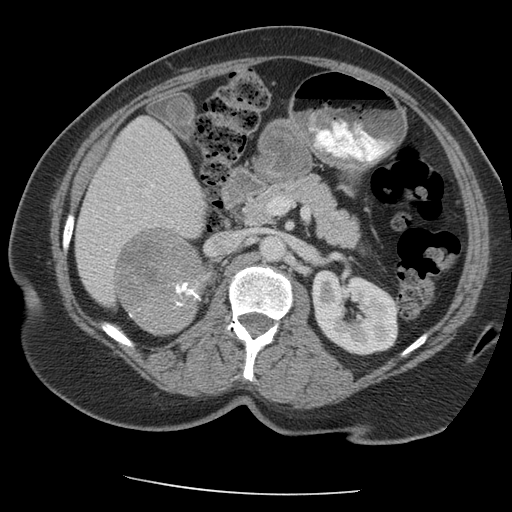
Contrast-enhanced abdominal CT, one axial slice; slice 115 of 163 in the series (ordered by position); reconstruction kernel STANDARD; intravenous contrast given; soft-tissue window (W 400 / L 40 HU); 2.5 mm slice thickness; 512 × 512 image matrix, field of view 360 × 360 mm. Female patient, age 70 years. From the clinical record (not read from this slice): diagnosis: adrenocortical carcinoma; tumour side: right adrenal; tumour size at pathology: 9.5 cm; Ki-67 index: 5 %; stage (as recorded): 2.
Annotated regions visible in this slice (semi-automatic segmentation, software-assisted and operator-edited):
- mass: box from (x=116, y=230) to (x=207, y=336) px